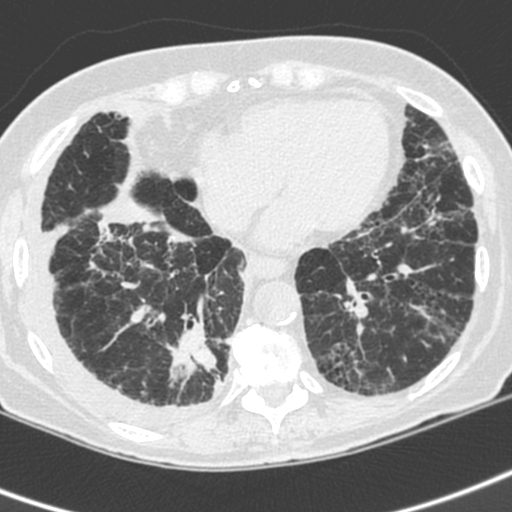
Low-dose screening chest CT, axial slice. First (baseline) screen. Lung window (W 1500 / L -600 HU). 1.3 mm slice thickness. Standard (soft-tissue) reconstruction kernel (C). 120 kVp. Female, age 73 years at enrolment. Current smoker at enrolment.
Expert-annotated lung lesion, bounding box [x1, y1, x2, y2] px = [154, 315, 234, 406]. Reader record for this screening exam (exam-level; its link to the box is not recorded): non-calcified nodule or mass ≥4 mm, right lower lobe, 35 × 30 mm, spiculated (stellate) margins, soft tissue attenuation. Official screen result: positive, change unspecified: nodule(s) >= 4 mm or enlarging nodule(s), mass(es), or other non-specific abnormalities suspicious for lung cancer.